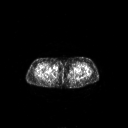
FDG PET of an extremity soft-tissue mass (from a PET/CT study), one axial slice. Position 242 of 311 along the scan axis. 128 × 128 image matrix, field of view 700 × 700 mm. Patient: female, 78 years. Case-level facts recorded for this patient, not image findings: histological type: leiomyosarcoma; grade: intermediate; site of the primary tumour: parascapusular.
Annotated regions visible in this slice (expert contour drawn on MRI and transferred to this co-registered scan by the dataset authors):
- gross tumour volume including surrounding oedema: bounding box <52,65,59,72> (left, top, right, bottom; pixels)
- gross tumour volume (mass): <53,65,59,71>